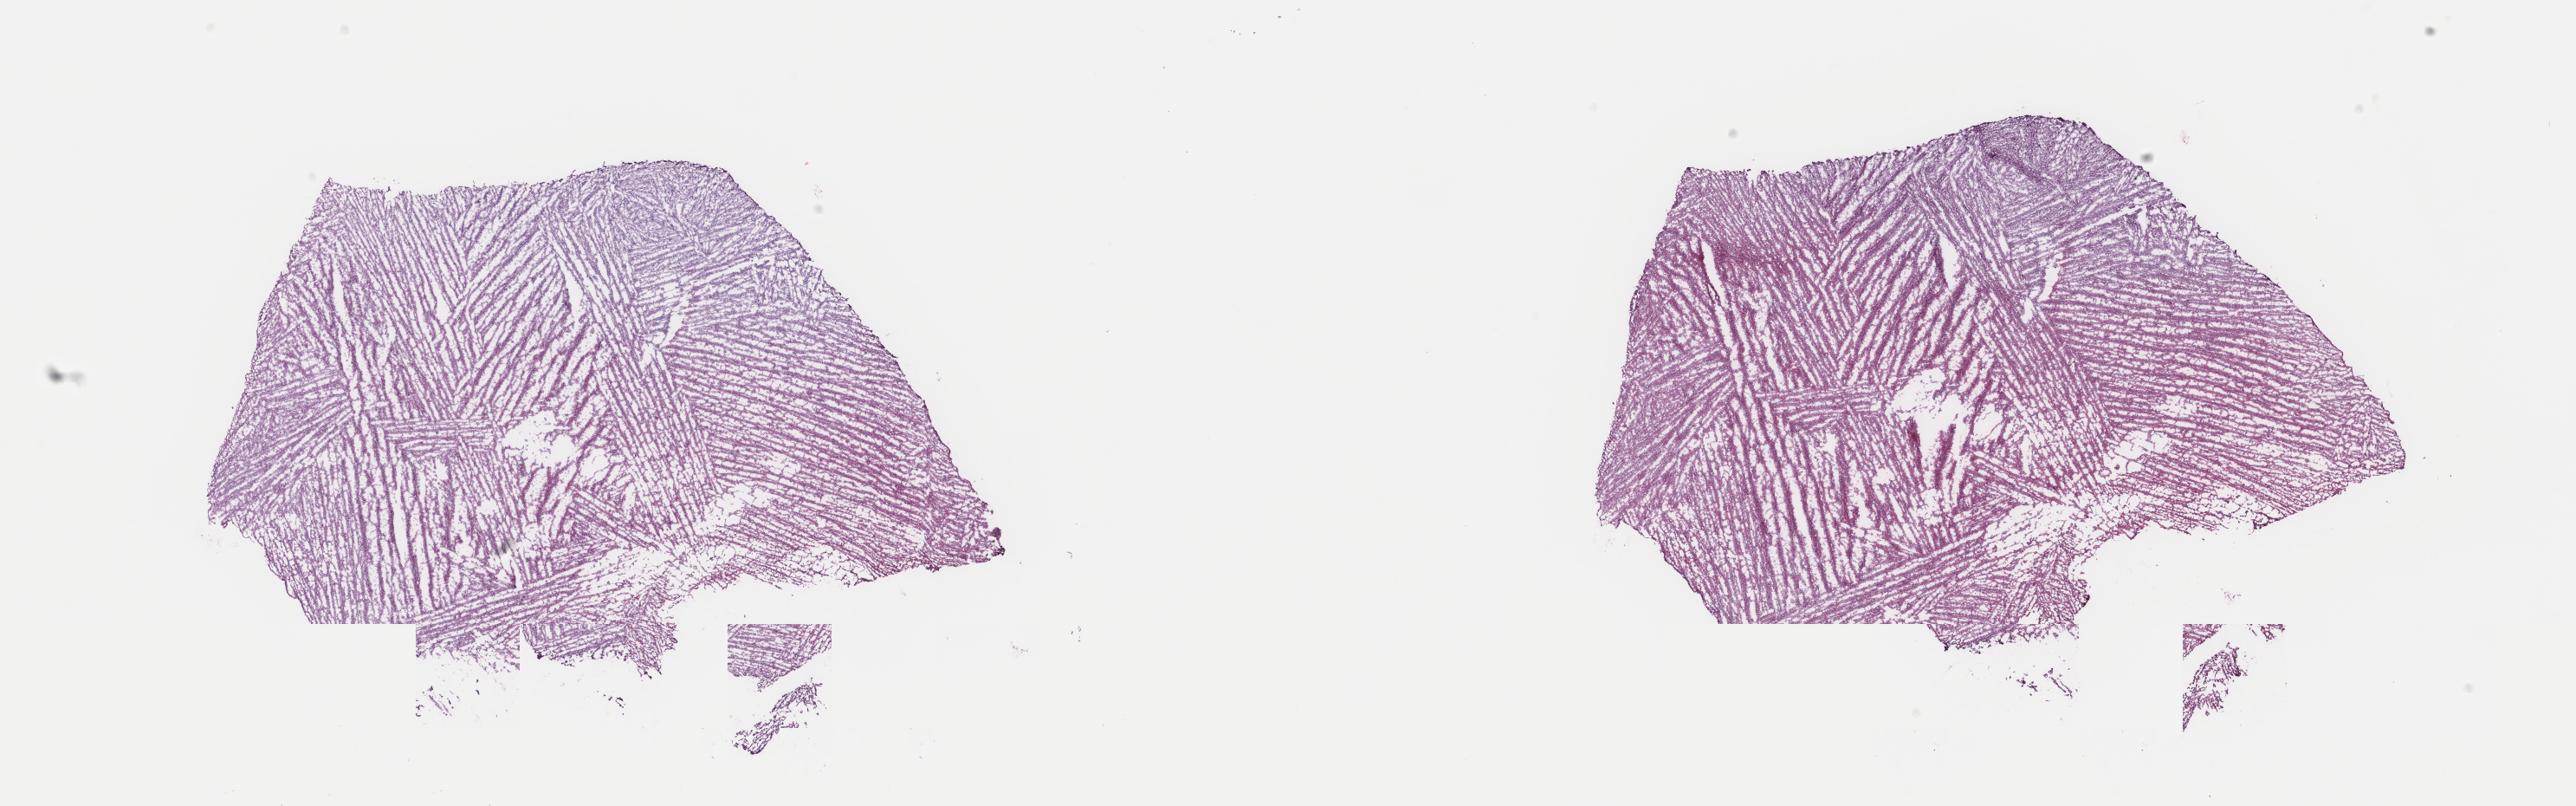
Digitized Hematoxylin and eosin (H&E) stained tissue section (whole slide) — whole scanned area (about 23.6 x 7.4 mm, acquisition: 40x scan) shown as a low-resolution overview; frozen section; primary tumour sample from the brain. Patient: female, age at initial diagnosis 25 years. Pathologist review of this section (percent, as recorded): tumour cells 60%, tumour nuclei 90%.
Pathologic diagnosis: Oligodendroglioma, NOS (cerebrum).